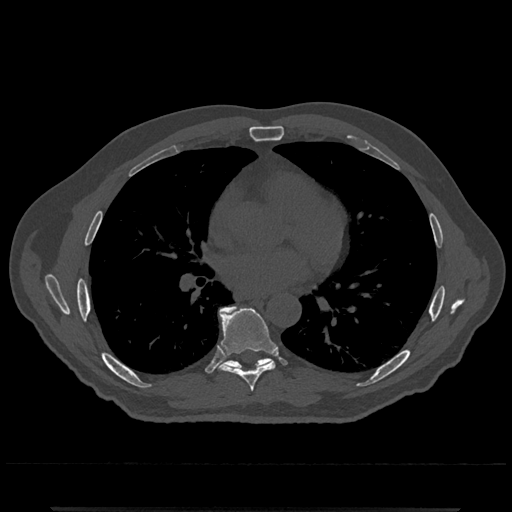
CT including the spine, one axial slice; position 706 of 797 along the scan axis; reconstruction kernel Br40s/3; 120 kVp; bone window (W 1800 / L 400 HU); 0.5 mm slice thickness; 512 × 512 image matrix, field of view 393 × 393 mm. Male patient, age 67 years. From the clinical record (not read from this slice): primary cancer: prostate.
Annotated regions visible in this slice (semi-automatic segmentation, software-assisted and operator-edited):
- T7 vertebra: bounding box <219,307,276,392> (left, top, right, bottom; pixels)
- T8 vertebra: <219,306,271,369>